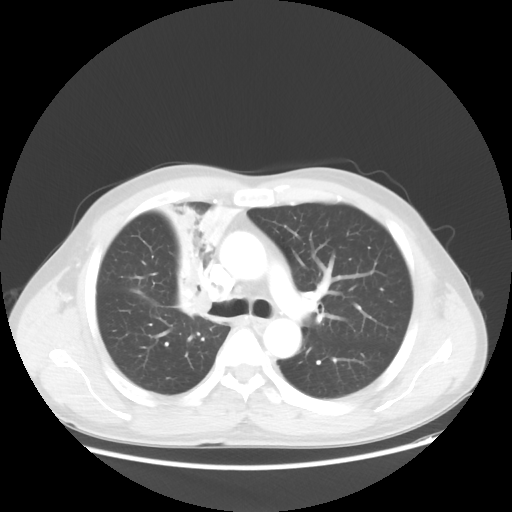
Chest CT, one axial slice; slice 35 of 56 in the series (ordered by position); reconstruction kernel STANDARD; 100 kVp; lung window (W 1500 / L -600 HU); 5 mm slice thickness; 512 × 512 image matrix, field of view 398 × 398 mm. Patient: male, 60 years. From the clinical record (not read from this slice): clinical TNM (as recorded): T2a N1 M0.
Annotated regions visible in this slice (rectangle marked by the reading radiologist):
- lung tumour (recorded histology: squamous cell carcinoma): bounding box <150,180,238,318> (left, top, right, bottom; pixels)